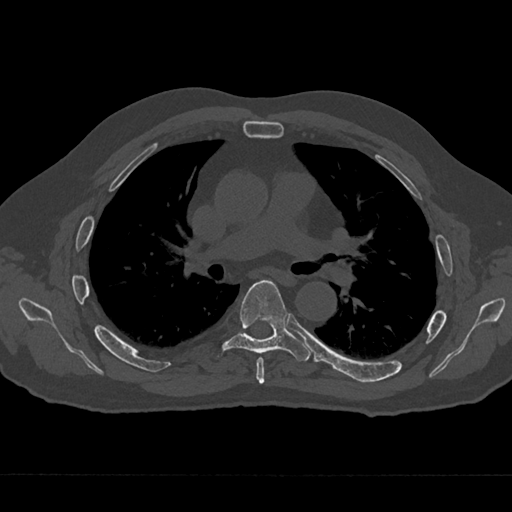
CT including the spine, one axial slice. Slice 431 of 797 in the series (ordered by position). 120 kVp. Bone window (W 1800 / L 400 HU). 0.5 mm slice thickness. 512 × 512 image matrix, field of view 377 × 377 mm. Patient: male, 75 years. From the clinical record (not read from this slice): primary cancer: renal; vertebrae with lytic lesions (as recorded): T4.
Annotated regions visible in this slice (semi-automatic segmentation, software-assisted and operator-edited):
- T5 vertebra: box from (x=256, y=357) to (x=265, y=384) px
- T6 vertebra: (x=218, y=280)–(x=310, y=362)